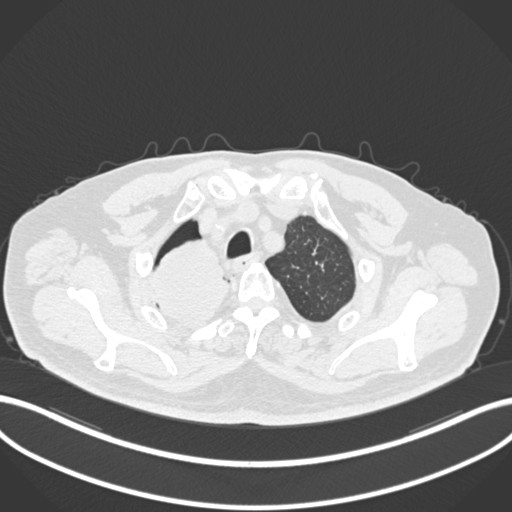
Chest CT, one axial slice; slice 183 of 218 in the series (ordered by position); reconstruction kernel B30f; 120 kVp; lung window (W 1500 / L -600 HU); 1 mm slice thickness; 512 × 512 image matrix. Male patient, age 68 years. From the clinical record (not read from this slice): clinical TNM (as recorded): T2a N0 M0.
Outlined on this slice (rectangle marked by the reading radiologist):
- lung tumour (recorded histology: adenocarcinoma): bounding box (x1, y1, x2, y2) in pixels: (145, 237, 233, 327)